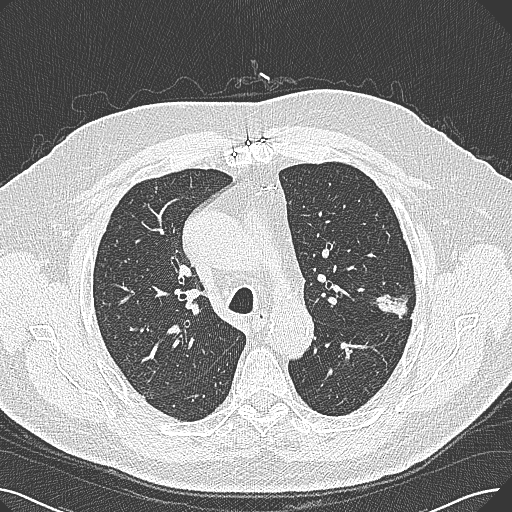
Chest CT (low-dose screening protocol), one axial image, baseline annual screen, lung window (W 1500 / L -600 HU), 1 mm slice thickness, lung (sharp) reconstruction kernel (B80f), slice 90 of 269 in the series. Male participant, aged 74 years at enrolment.
Expert reader's lesion annotation, bounding box [x1, y1, x2, y2] px = [367, 273, 426, 324]. Screening reader's record for this exam (one nodule recorded; not confirmed to be the boxed lesion): non-calcified nodule or mass ≥4 mm, left upper lobe, 15 × 10 mm, poorly defined margins, soft tissue attenuation. Official screen result: positive, change unspecified: nodule(s) >= 4 mm or enlarging nodule(s), mass(es), or other non-specific abnormalities suspicious for lung cancer. Lung cancer was diagnosed 124 days after this screen: adenocarcinoma, NOS, left upper lobe, well differentiated (G1), stage IA (AJCC 6th edition), 26 mm at pathology.